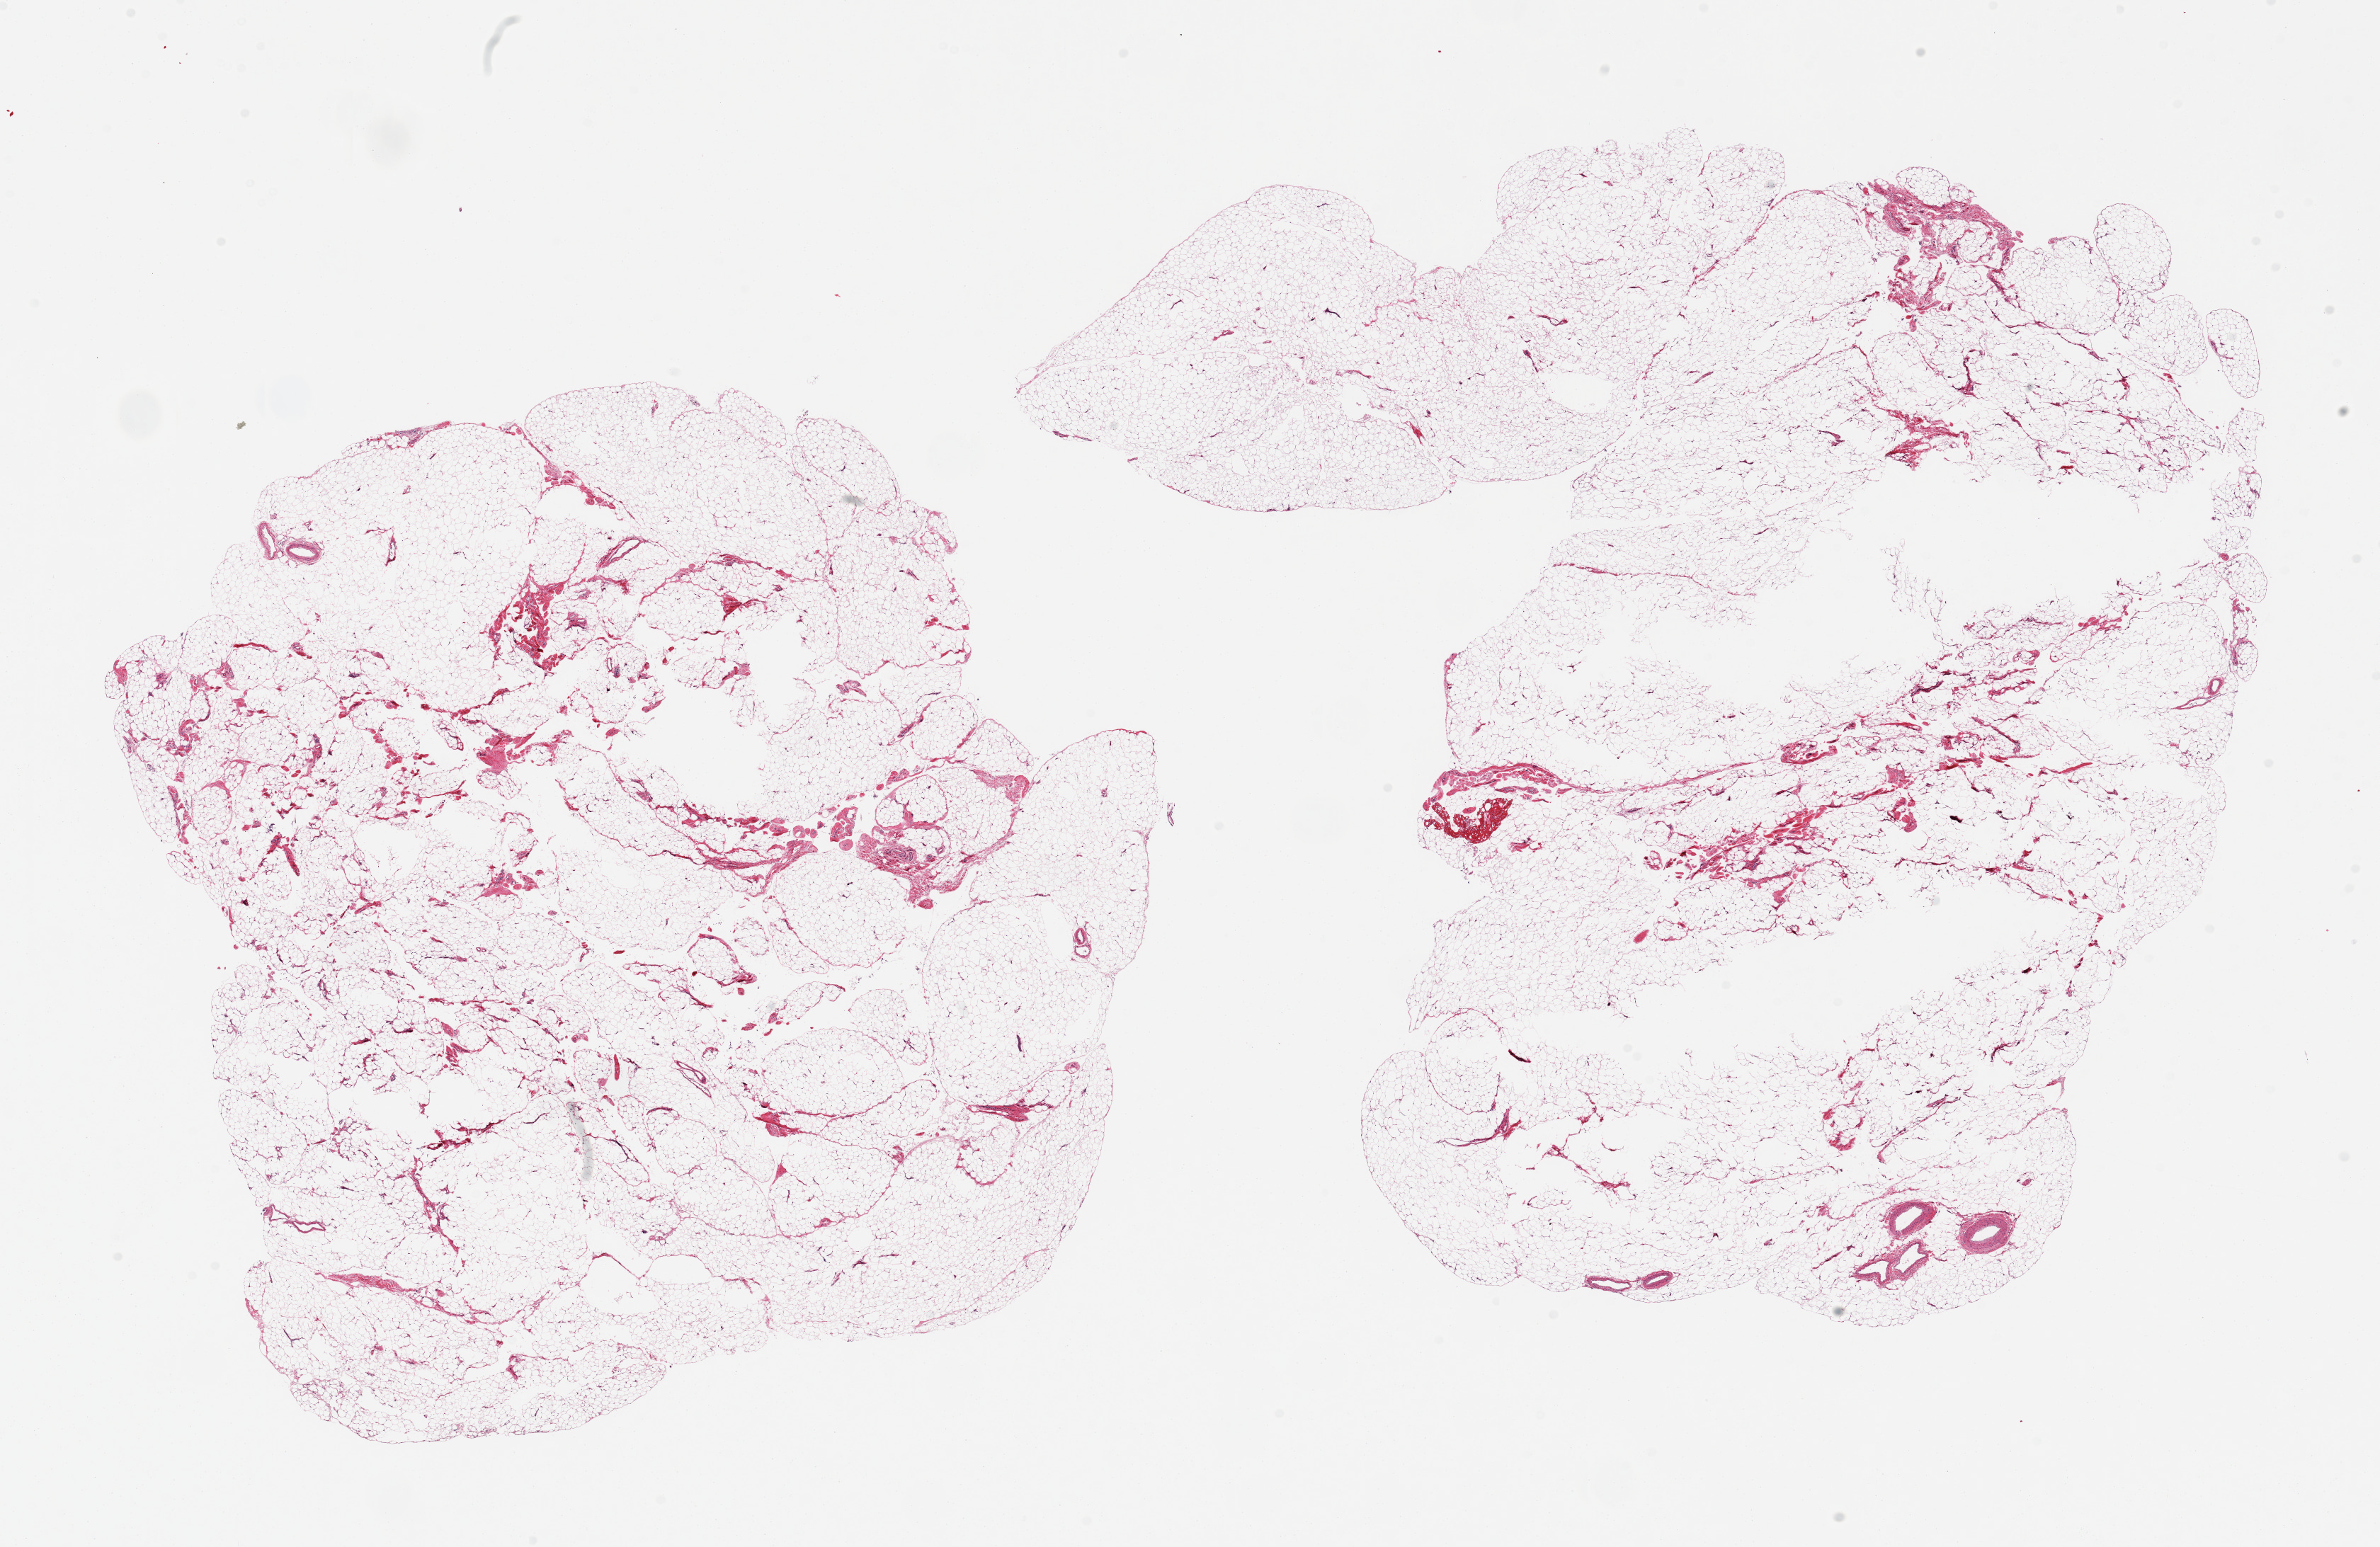
Hematoxylin and eosin (H&E) whole-slide image, brightfield, a low-resolution overview of the entire scanned area, about 26.6 x 17.3 mm, PAXgene-fixed, paraffin-embedded tissue, target tissue: omentum, tissue donor sample. Donor: female.
Pathologist's review note for this sample: 2 pieces; <5% fibrovascular content.